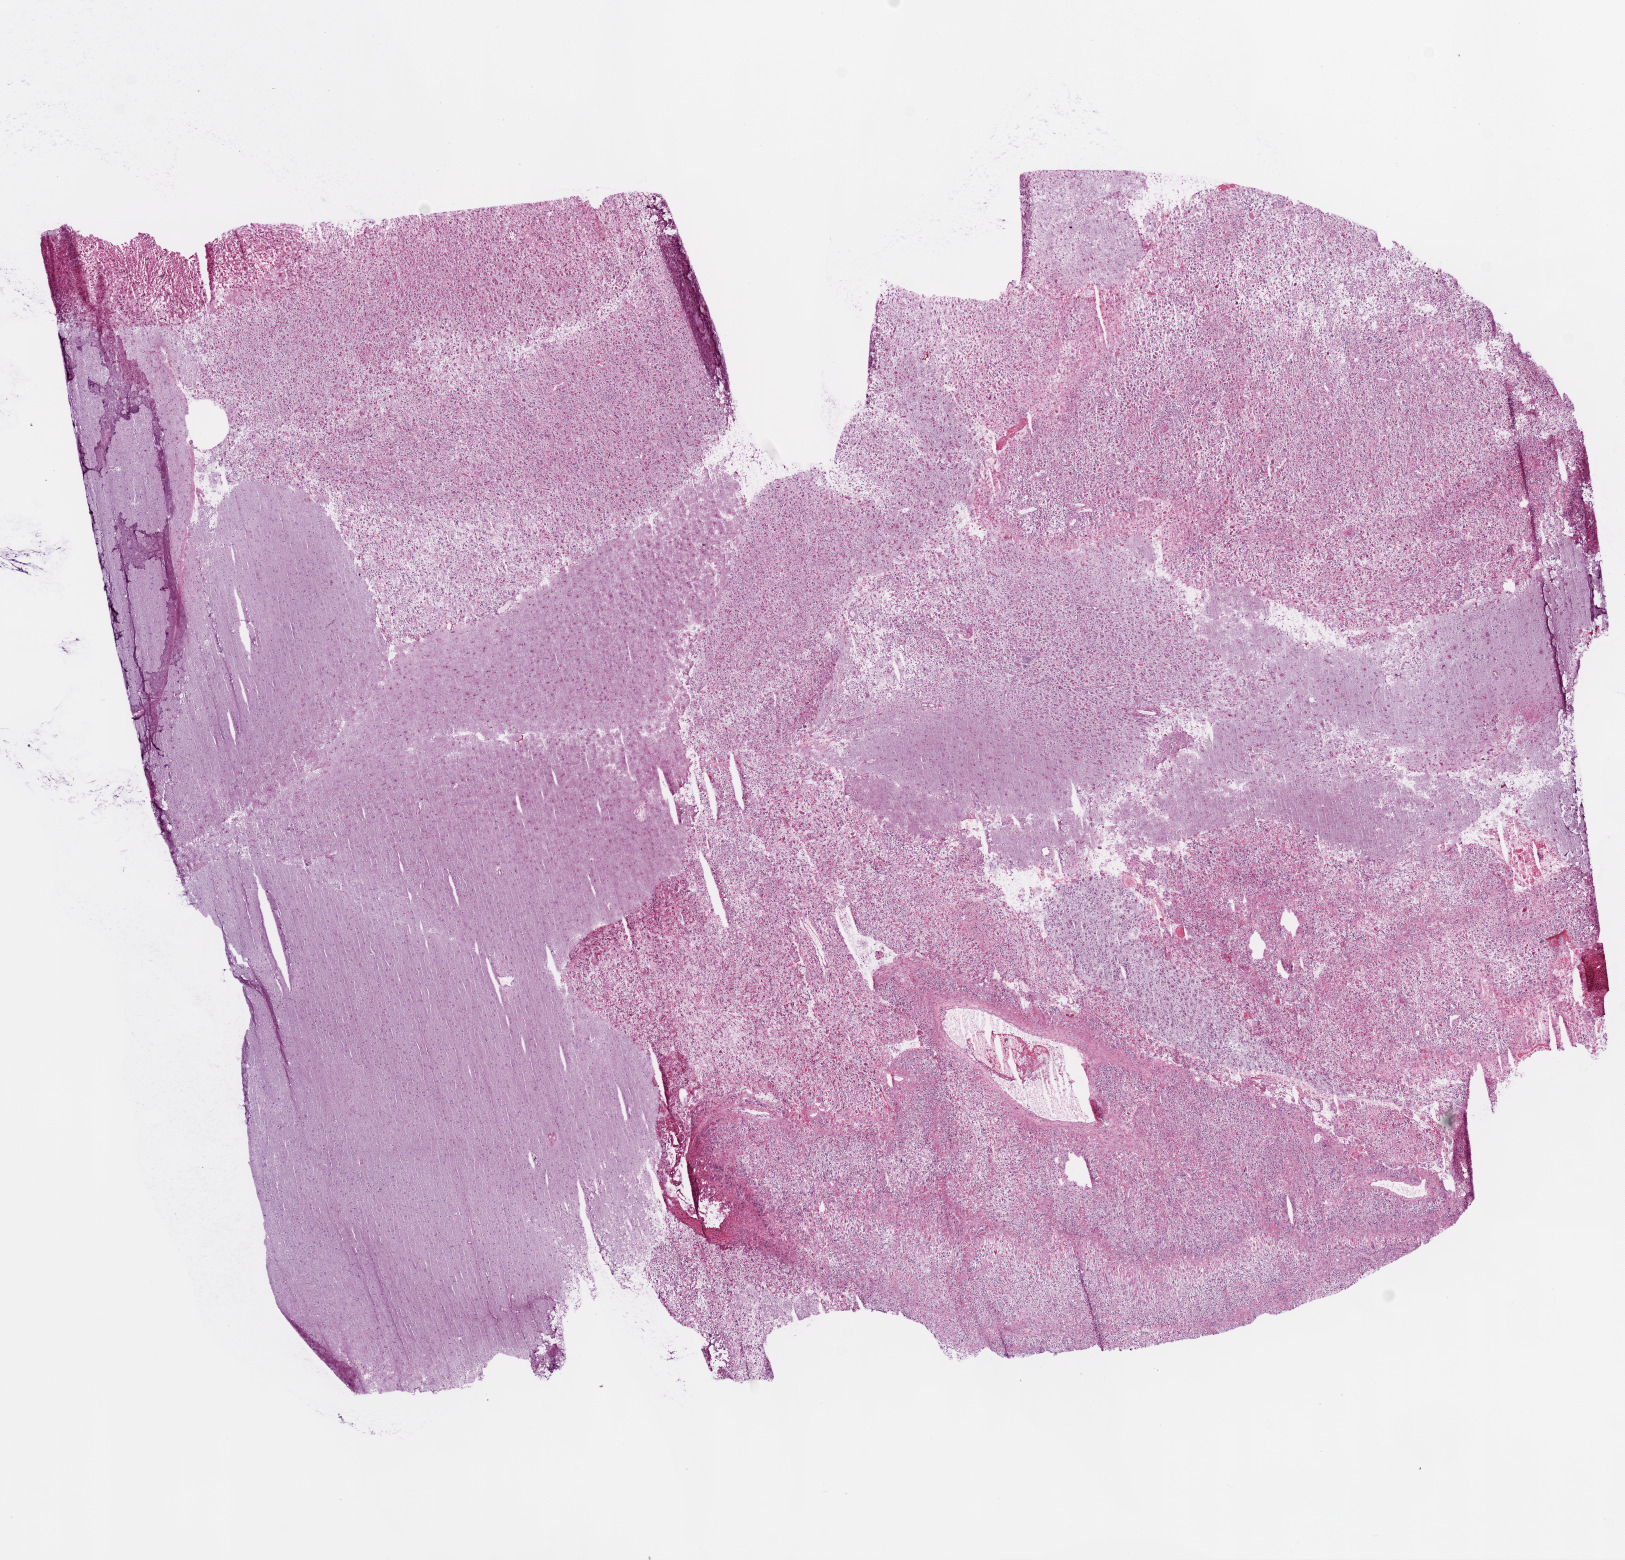
Whole-slide histology image, Hematoxylin and eosin (H&E) stained, whole scanned area (about 13.0 x 12.5 mm) shown as a low-resolution overview. Frozen section. Primary tumour sample from the brain. Female, age 53 years at initial diagnosis. Composition of this section per pathologist review: tumour cells 98%, tumour nuclei 80%, normal cells 0%, stromal cells 0%, necrosis 2%.
- histologic diagnosis: Glioblastoma